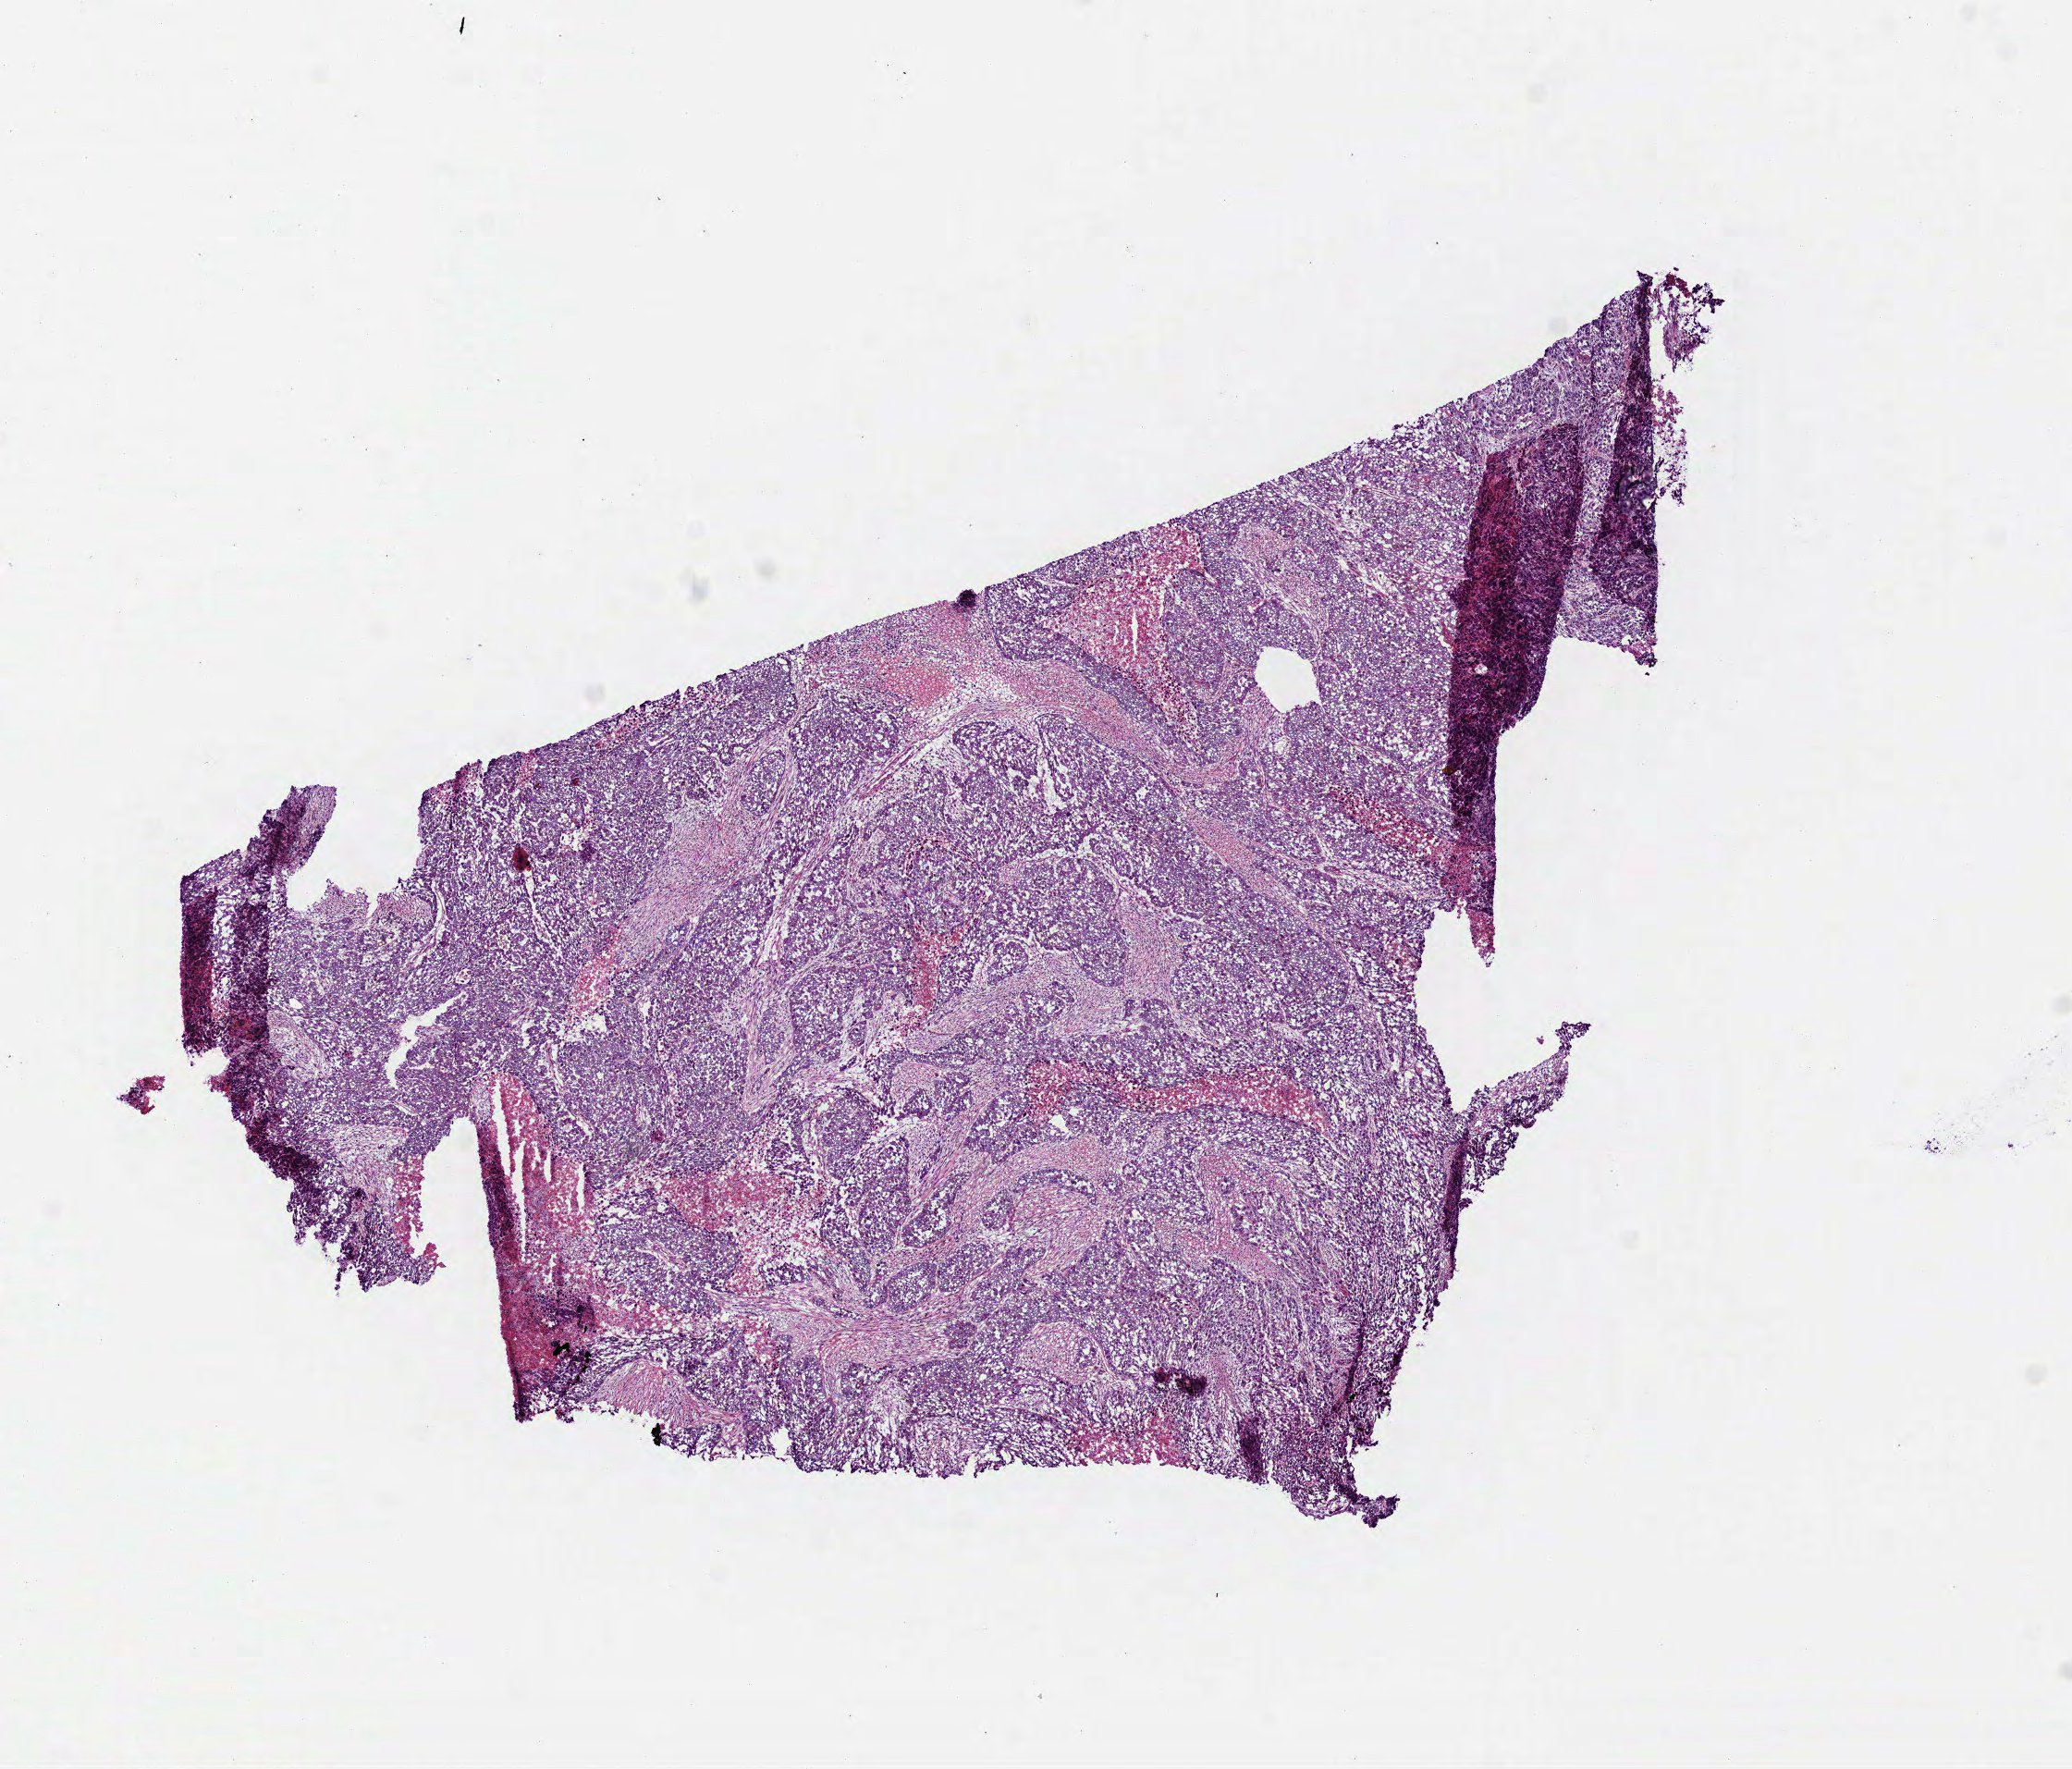
Digitized Hematoxylin and eosin (H&E) stained tissue section (whole slide) — low-resolution overview of the scanned area, about 9.0 x 7.7 mm (acquisition: 40x scan), frozen section from the bottom of the tissue portion, lung, primary tumour sample. Patient: male, age at initial diagnosis 68 years. Pathologist review of this section (percent, as recorded): tumour cells 80%, tumour nuclei 70%, normal cells 0%, stromal cells 15%, necrosis 5%.
TNM: T2 N1 M0. AJCC pathologic stage: IIB (6th edition). Diagnosis: Squamous cell carcinoma, NOS. Laterality: right.